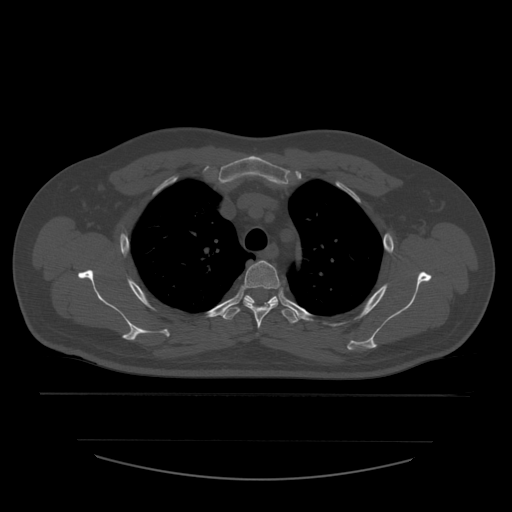
CT including the spine, one axial slice. Position 428 of 532 along the scan axis. 120 kVp. Bone window (W 1800 / L 400 HU). 1.25 mm slice thickness. 512 × 512 image matrix, field of view 441 × 441 mm. Patient age 44 years. Case-level facts recorded for this patient, not image findings: primary cancer: soft tissue sarcoma.
Structures marked on this image (semi-automatically segmented with operator editing):
- T3 vertebra: bounding box <243,260,281,329> (left, top, right, bottom; pixels)
- T4 vertebra: <222,295,299,324>